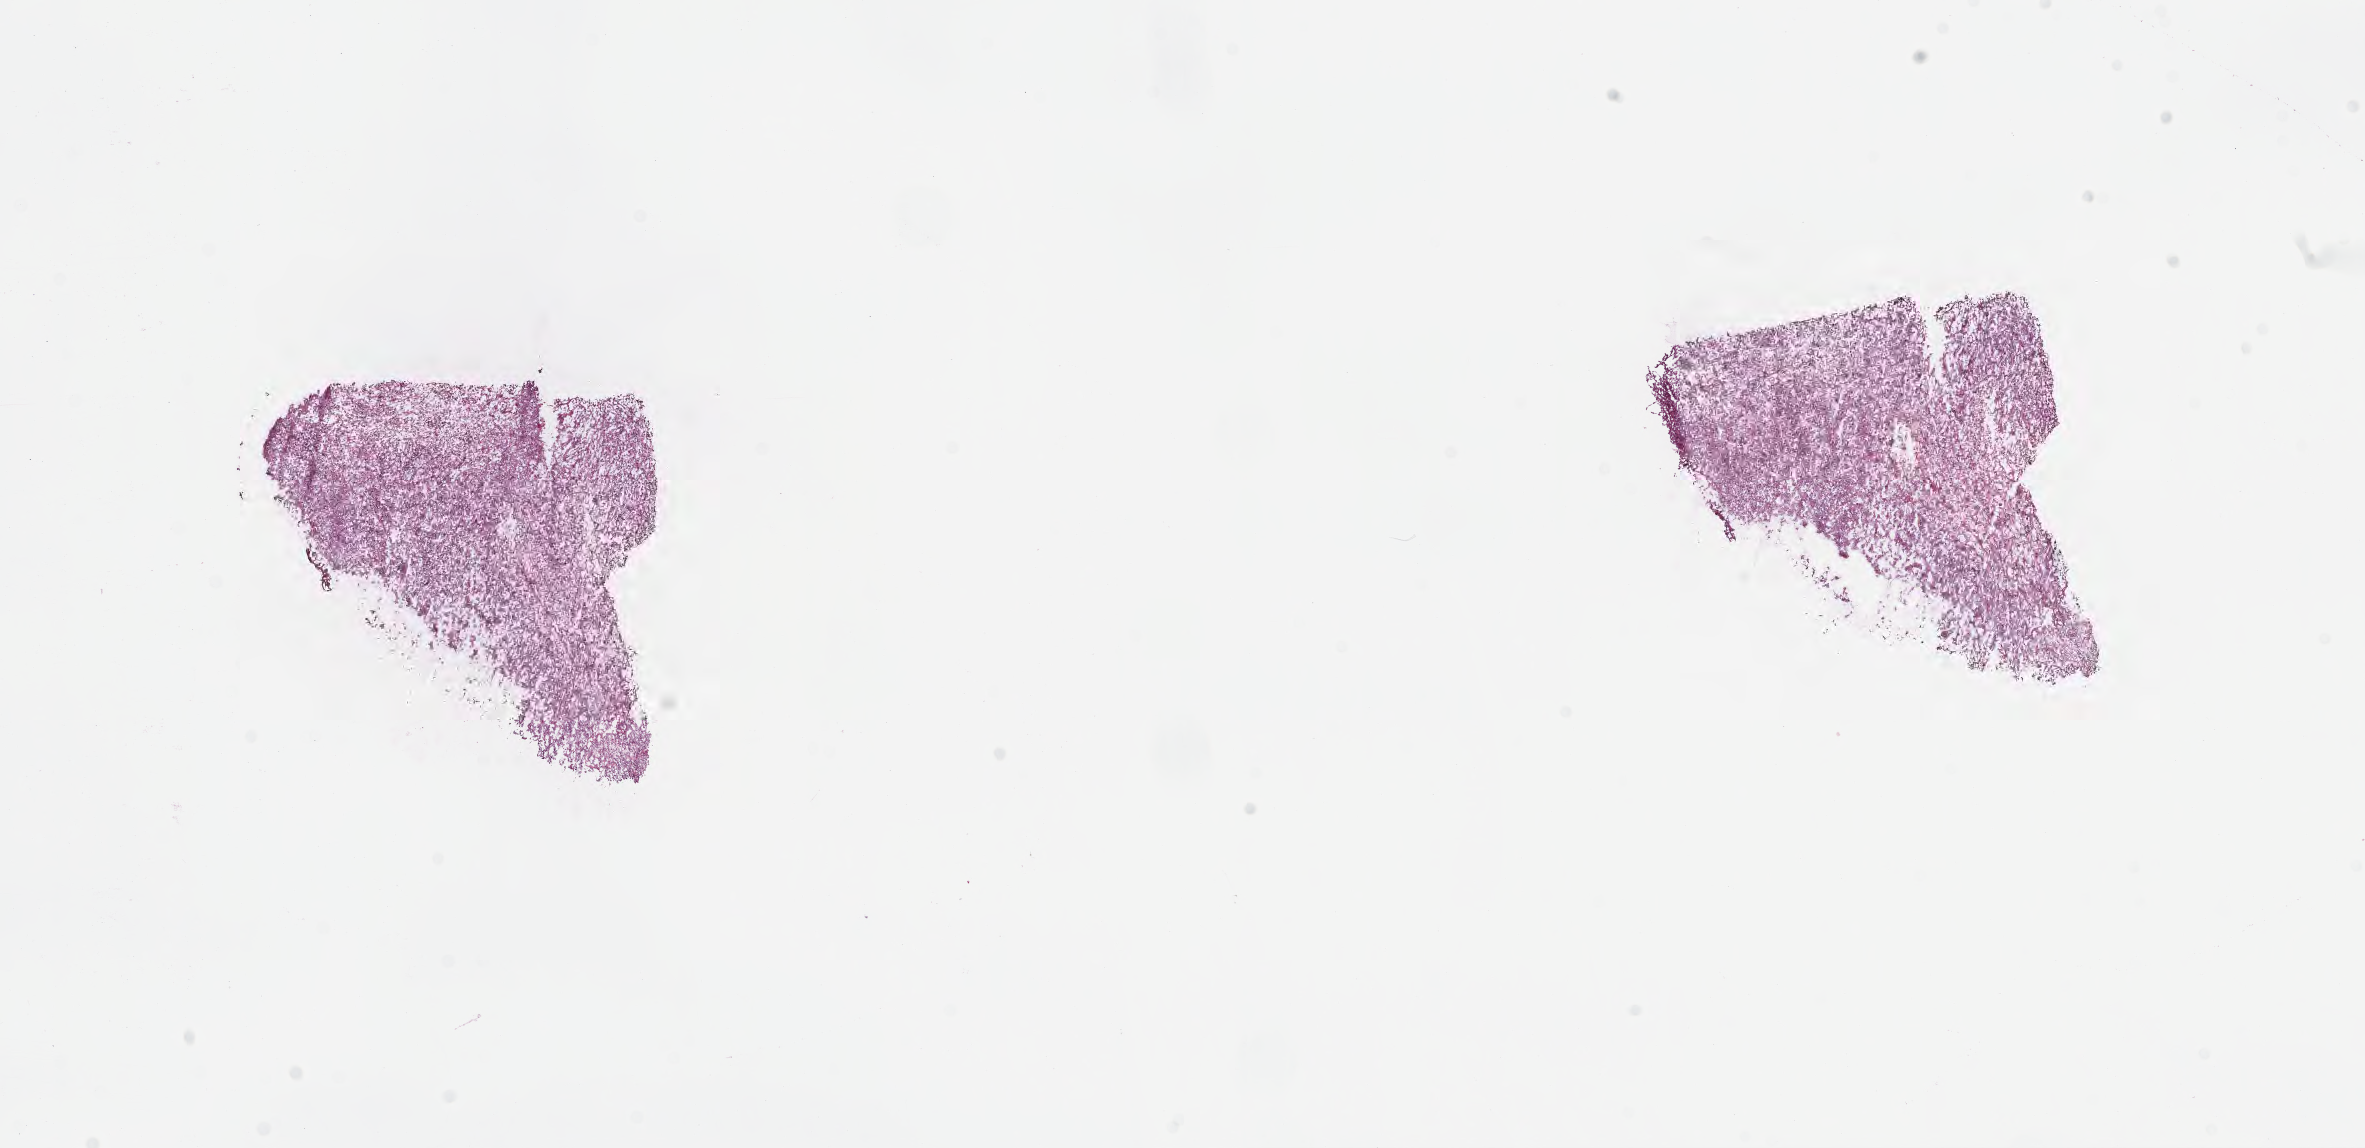
Whole-slide image, H&E stain — shown as a low-resolution overview of the whole scanned area (about 19.1 x 9.3 mm), frozen section (tissue freezing medium), specimen: metastatic tumor tissue, resected from lymph node. Male, age 69 years at initial diagnosis. Pathologist review of this section (percent, as recorded): tumor cells 69%, tumor nuclei 78%, stromal cells 12%, necrosis 0%, normal cells 19%. Infiltration values recorded for this section: lymphocyte infiltration 1%, monocyte infiltration 2%, neutrophil infiltration 0%.
Section: bottom of the tissue portion. Patient diagnosis (primary): Malignant melanoma, NOS.